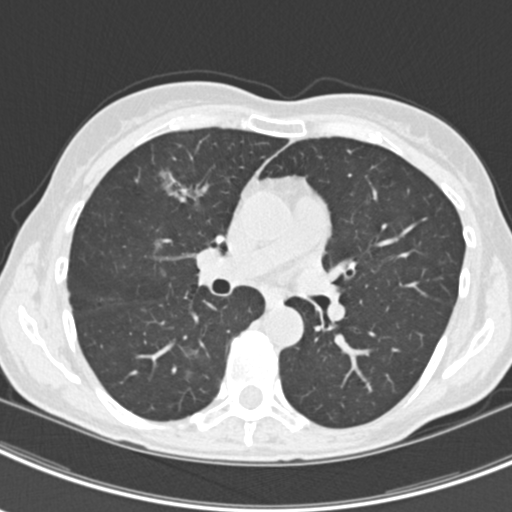
Low-dose screening chest CT, axial slice. Second screening round (one year after baseline). Lung window (W 1500 / L -600 HU). 2 mm slice thickness. 120 kVp. 512 × 512 image matrix. Female participant, aged 63 years at enrolment. Current smoker at enrolment.
Lesion marked by an expert reader, bounding box (x1, y1, x2, y2) in pixels: (157, 159, 216, 212). The screening reader recorded 9 non-calcified nodules or masses ≥4 mm on this exam (left upper lobe, right upper lobe, left upper lobe, left lower lobe, right middle lobe, left lower lobe, left lower lobe, right lower lobe, right lower lobe); which of them this box marks is not recorded. Lung cancer was diagnosed 408 days after this screen: bronchiolo-alveolar adenocarcinoma, NOS, right upper lobe, right middle lobe, right lower lobe, left upper lobe, left lower lobe, moderately differentiated (G2), stage IV (AJCC 6th edition).